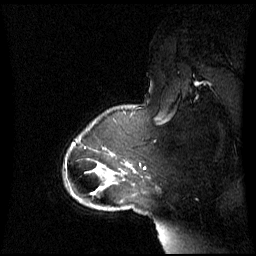
Breast MRI (dynamic contrast-enhanced), one sagittal slice; dynamic contrast-enhanced series, image 2 of 3 at this slice position (ordered by acquisition); 1.5 T; TE 4.2 ms, TR 8.4 ms; 2.8 mm slice thickness; 256 × 256 image matrix, field of view 270 × 270 mm. Patient: female, 43 years. From the clinical record (not read from this slice): setting: breast cancer imaged before/during neoadjuvant chemotherapy; receptor status: triple-negative.
Outlined on this slice (semi-automatic segmentation, software-assisted and operator-edited):
- analysis volume of interest (the breast-tissue region the enhancement analysis was run in; not a lesion): box from (x=65, y=118) to (x=143, y=198) px
- tumour enhancement mask (voxels above the 70 % enhancement threshold inside the analysis volume of interest): (x=92, y=162)–(x=128, y=194)